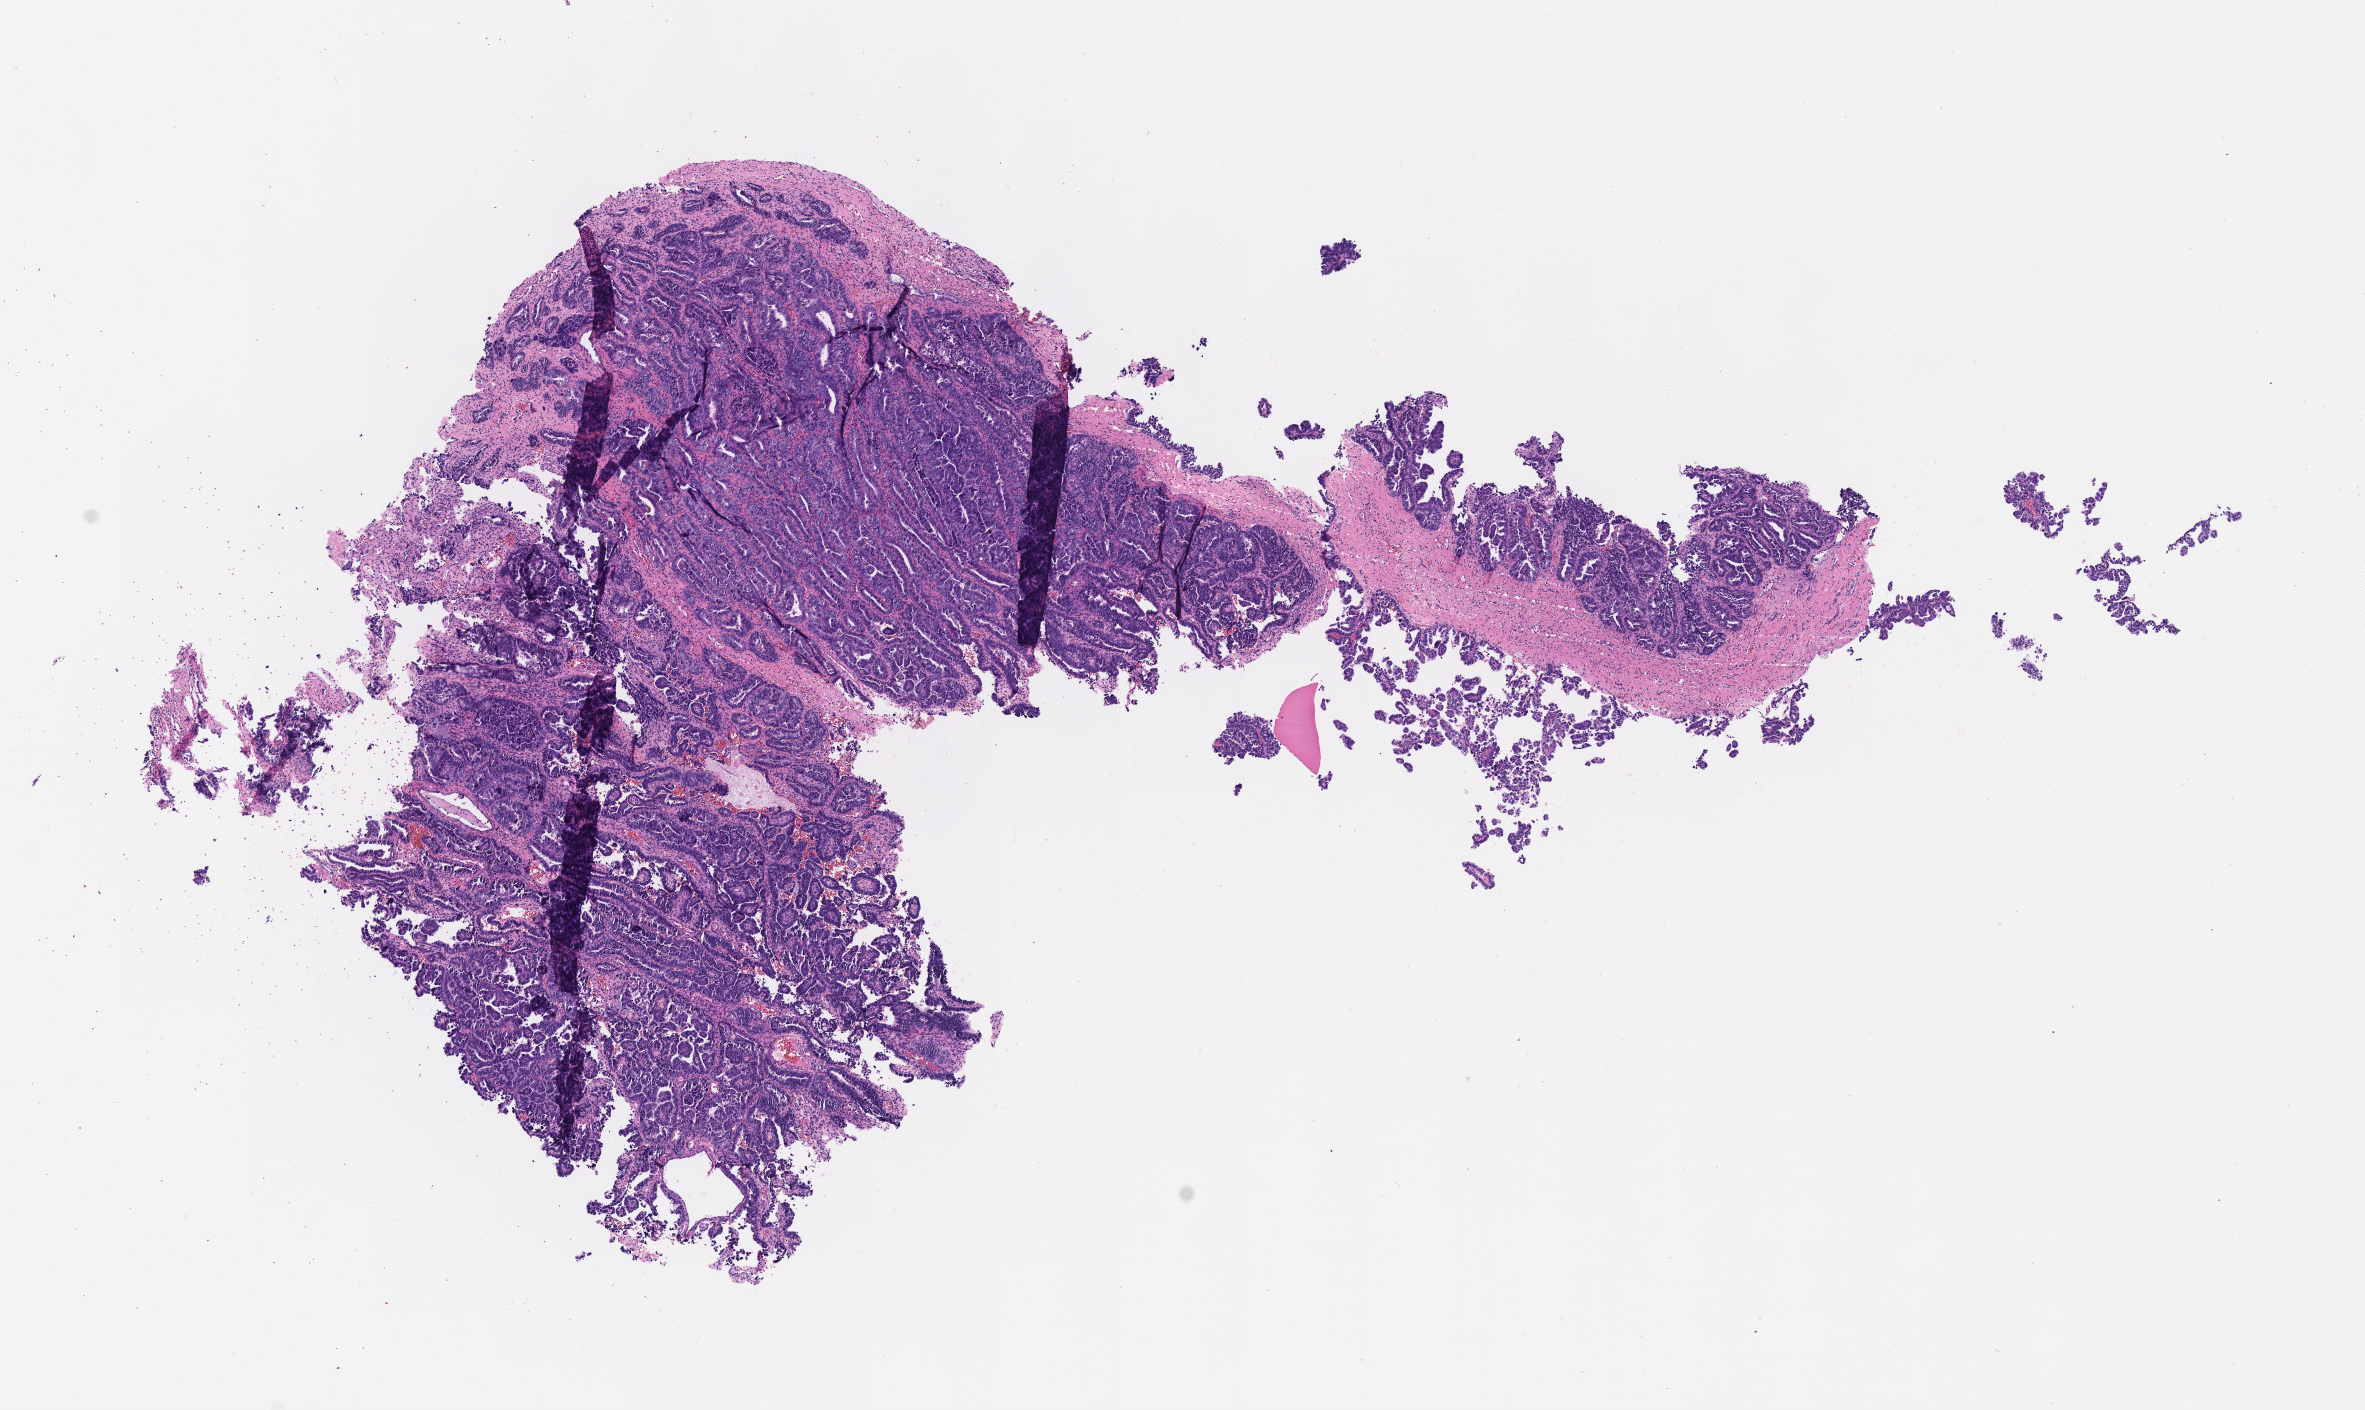
Digitized haematoxylin and eosin-stained section — whole scanned area (about 9.6 x 5.7 mm) shown as a low-resolution overview, specimen: tumor tissue, site: cervix. Patient female; aged 70.
Diagnosis: Adenocarcinoma, NOS.